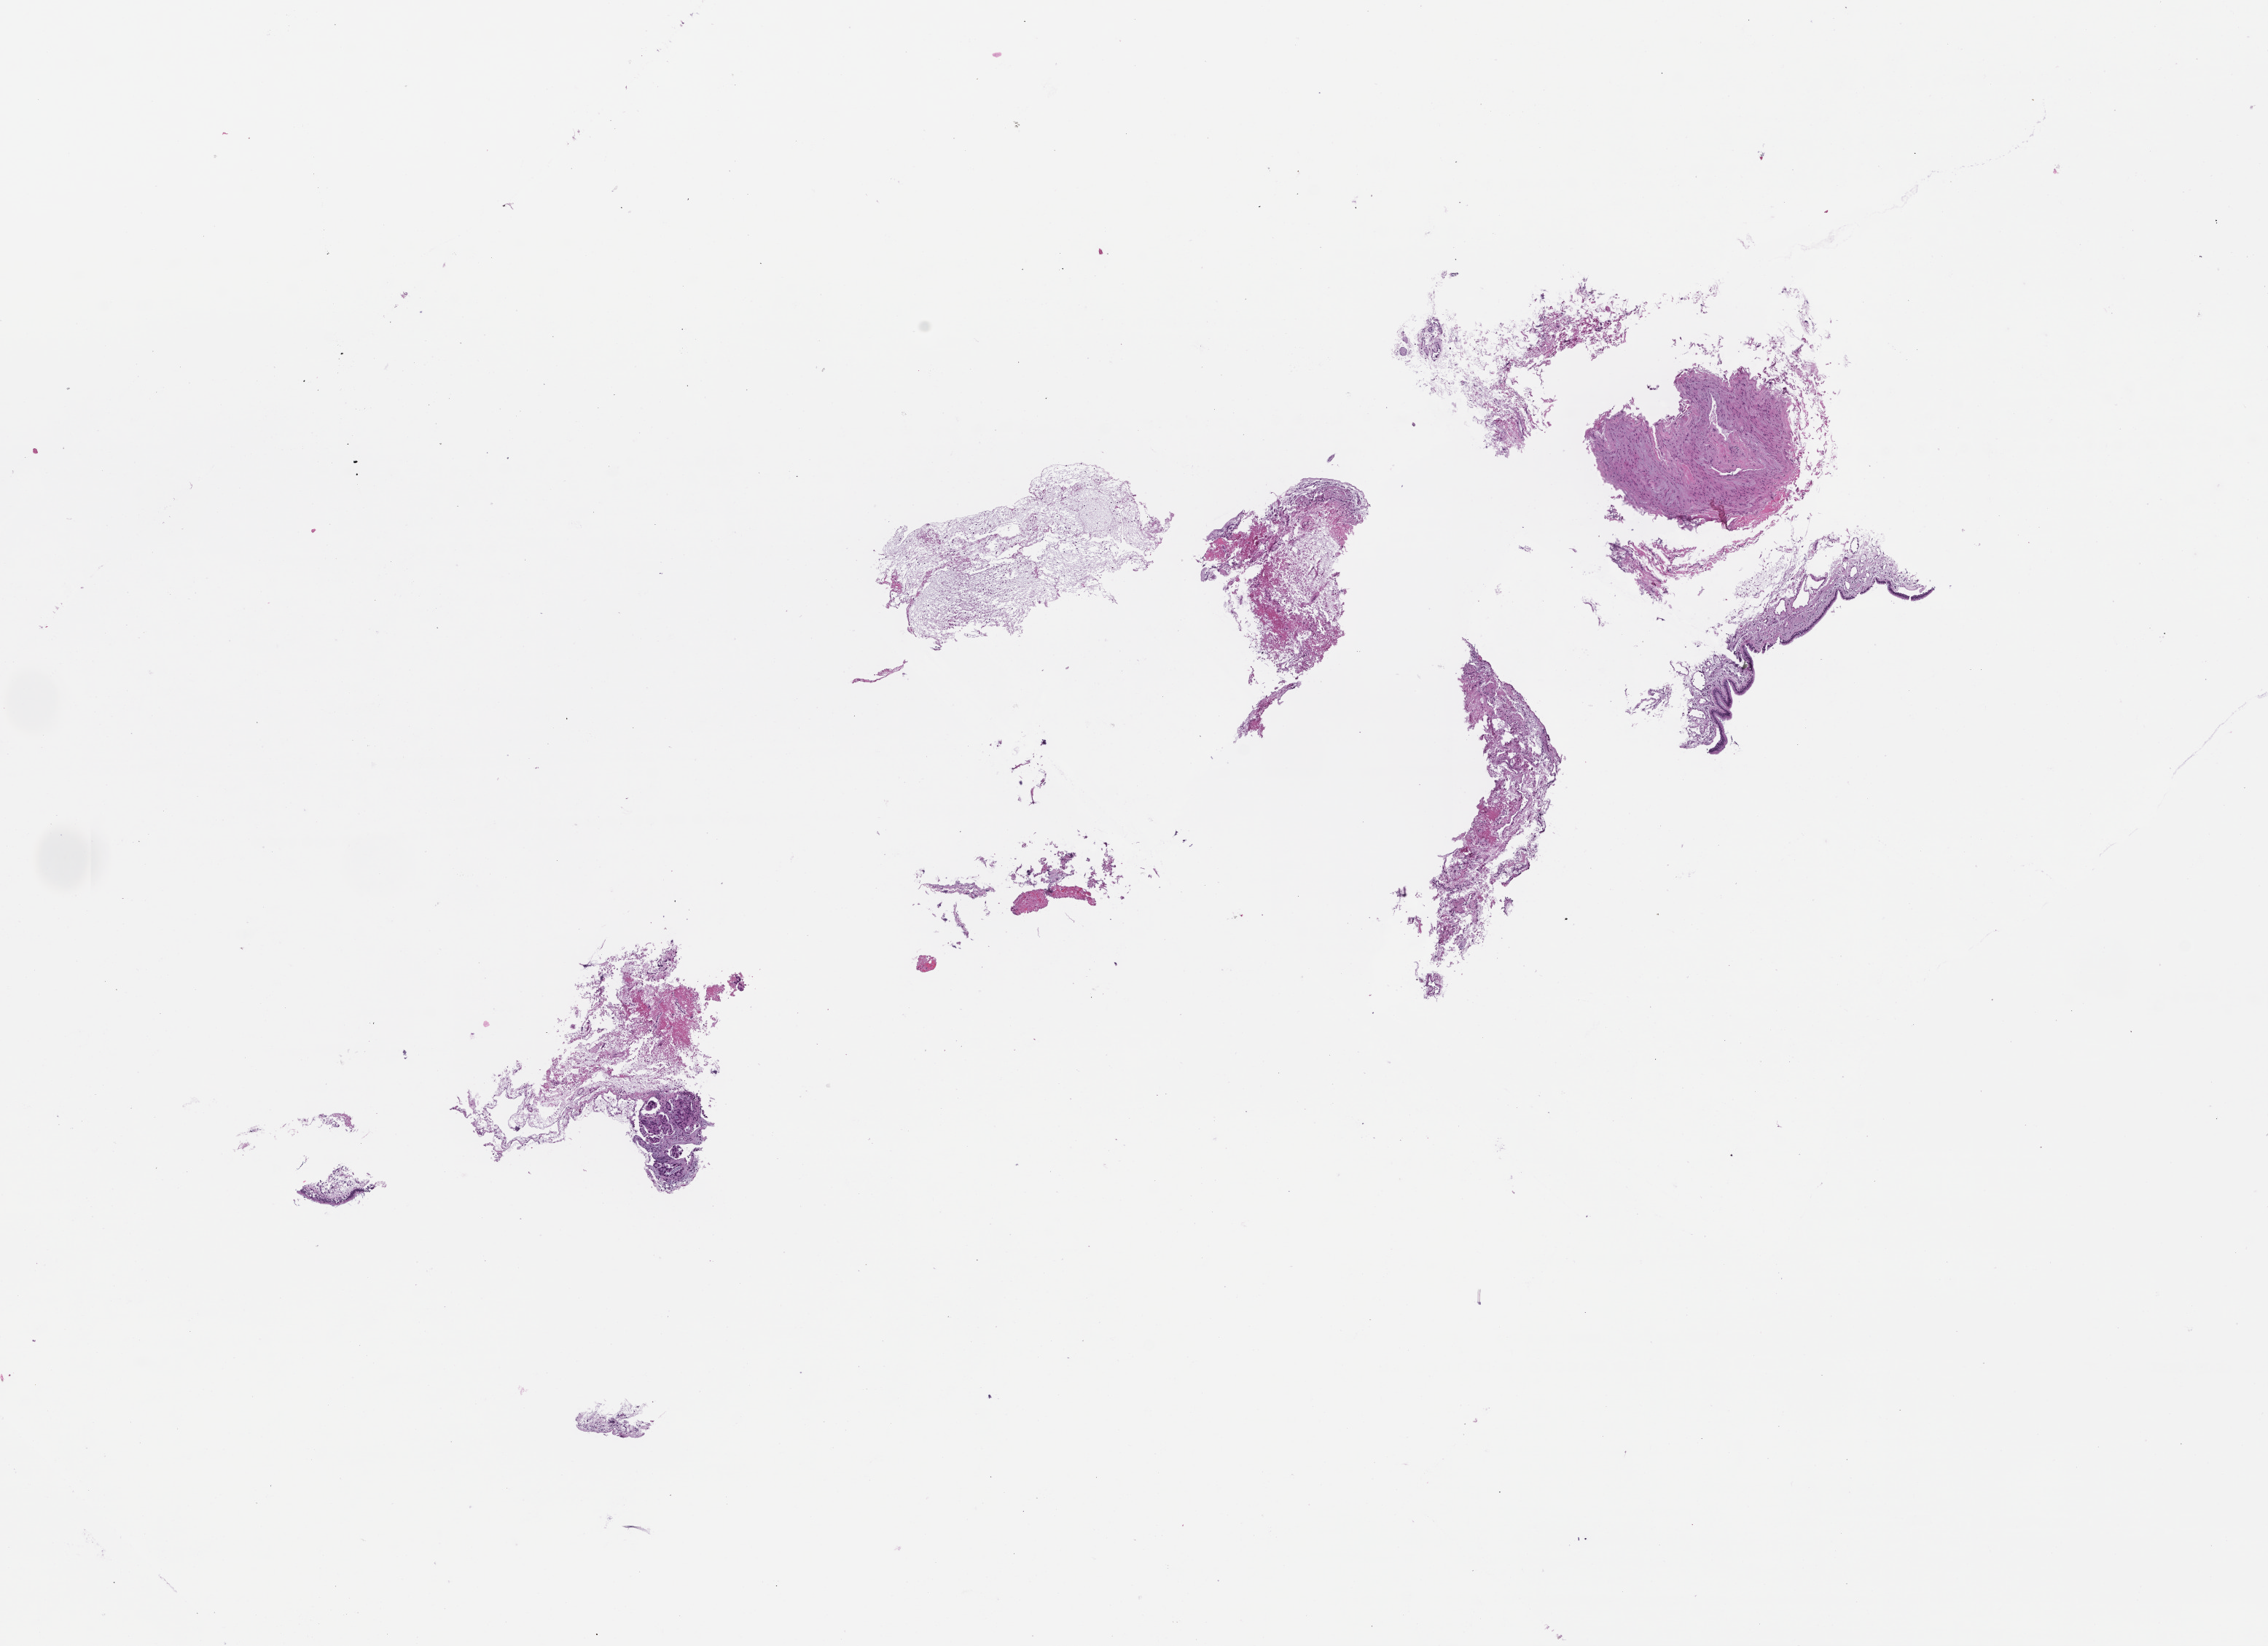
Digitized hematoxylin and eosin (H&E)-stained section — whole scanned area (about 12.6 x 9.1 mm) shown as a low-resolution overview, FFPE section, site: breast, archival tissue. Patient sex: female.
This section: primary tumour tissue. Diagnosis: Invasive Breast Carcinoma.